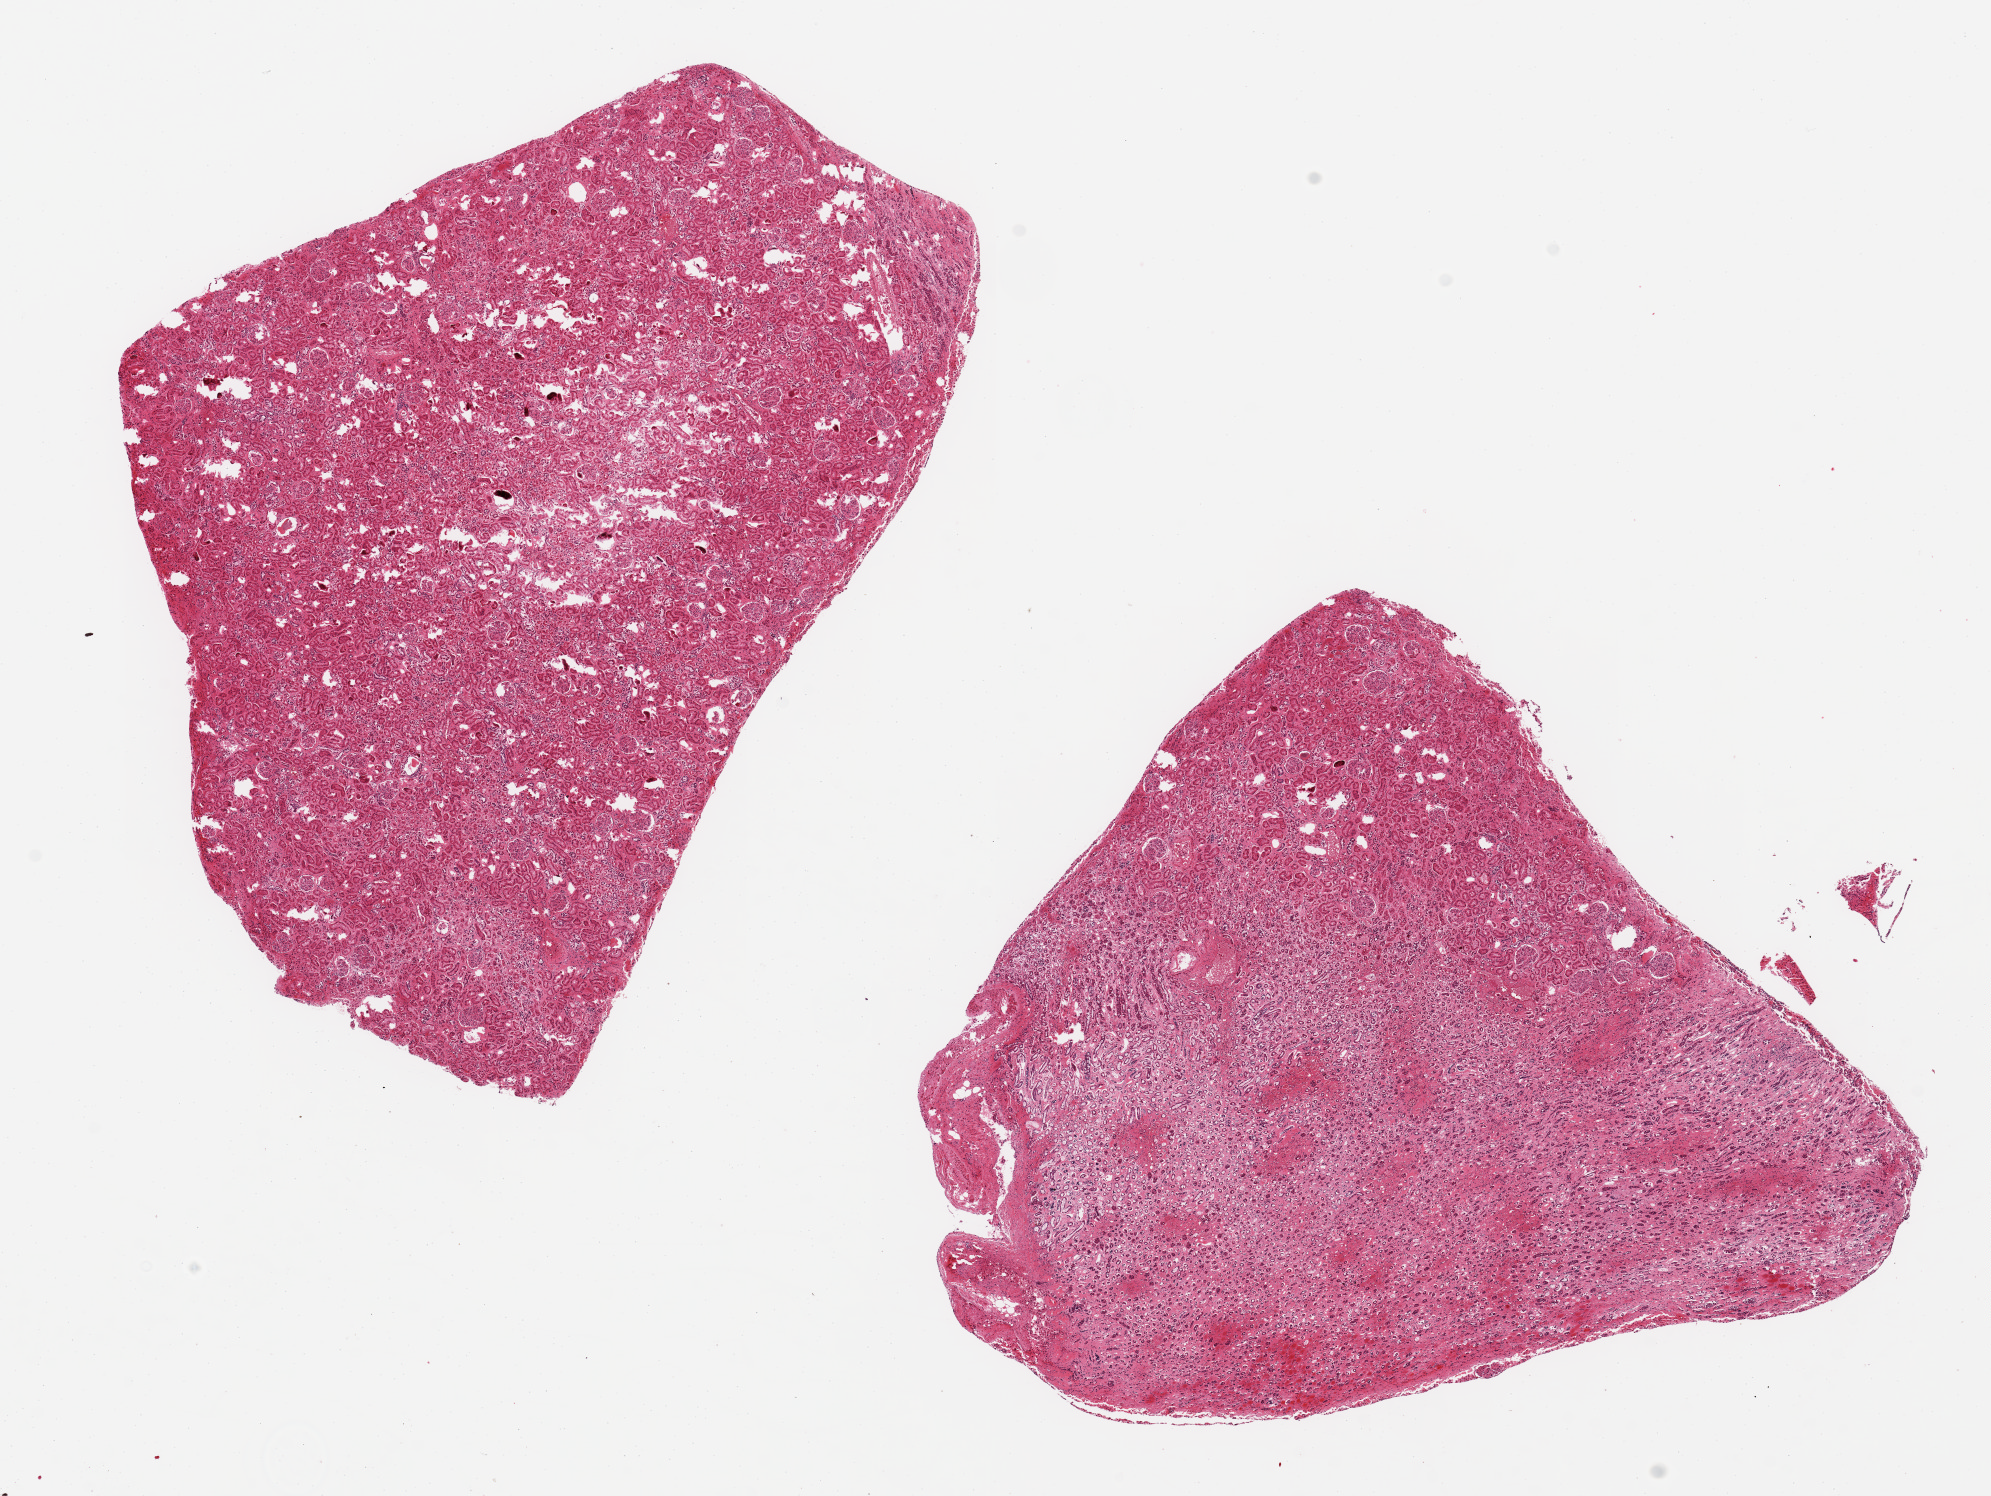
Whole-slide image, haematoxylin and eosin stain, shown as a low-resolution overview of the whole scanned area (about 15.8 x 11.8 mm, acquisition: 20x scan). PAXgene-fixed, paraffin-embedded tissue. Target tissue: renal medulla. Tissue donor sample. Donor sex: female.
- pathologist's review note for this sample: 2 ~6.5x6mm pieces, both with numerous glomeruli (50% or more of both aliquots)